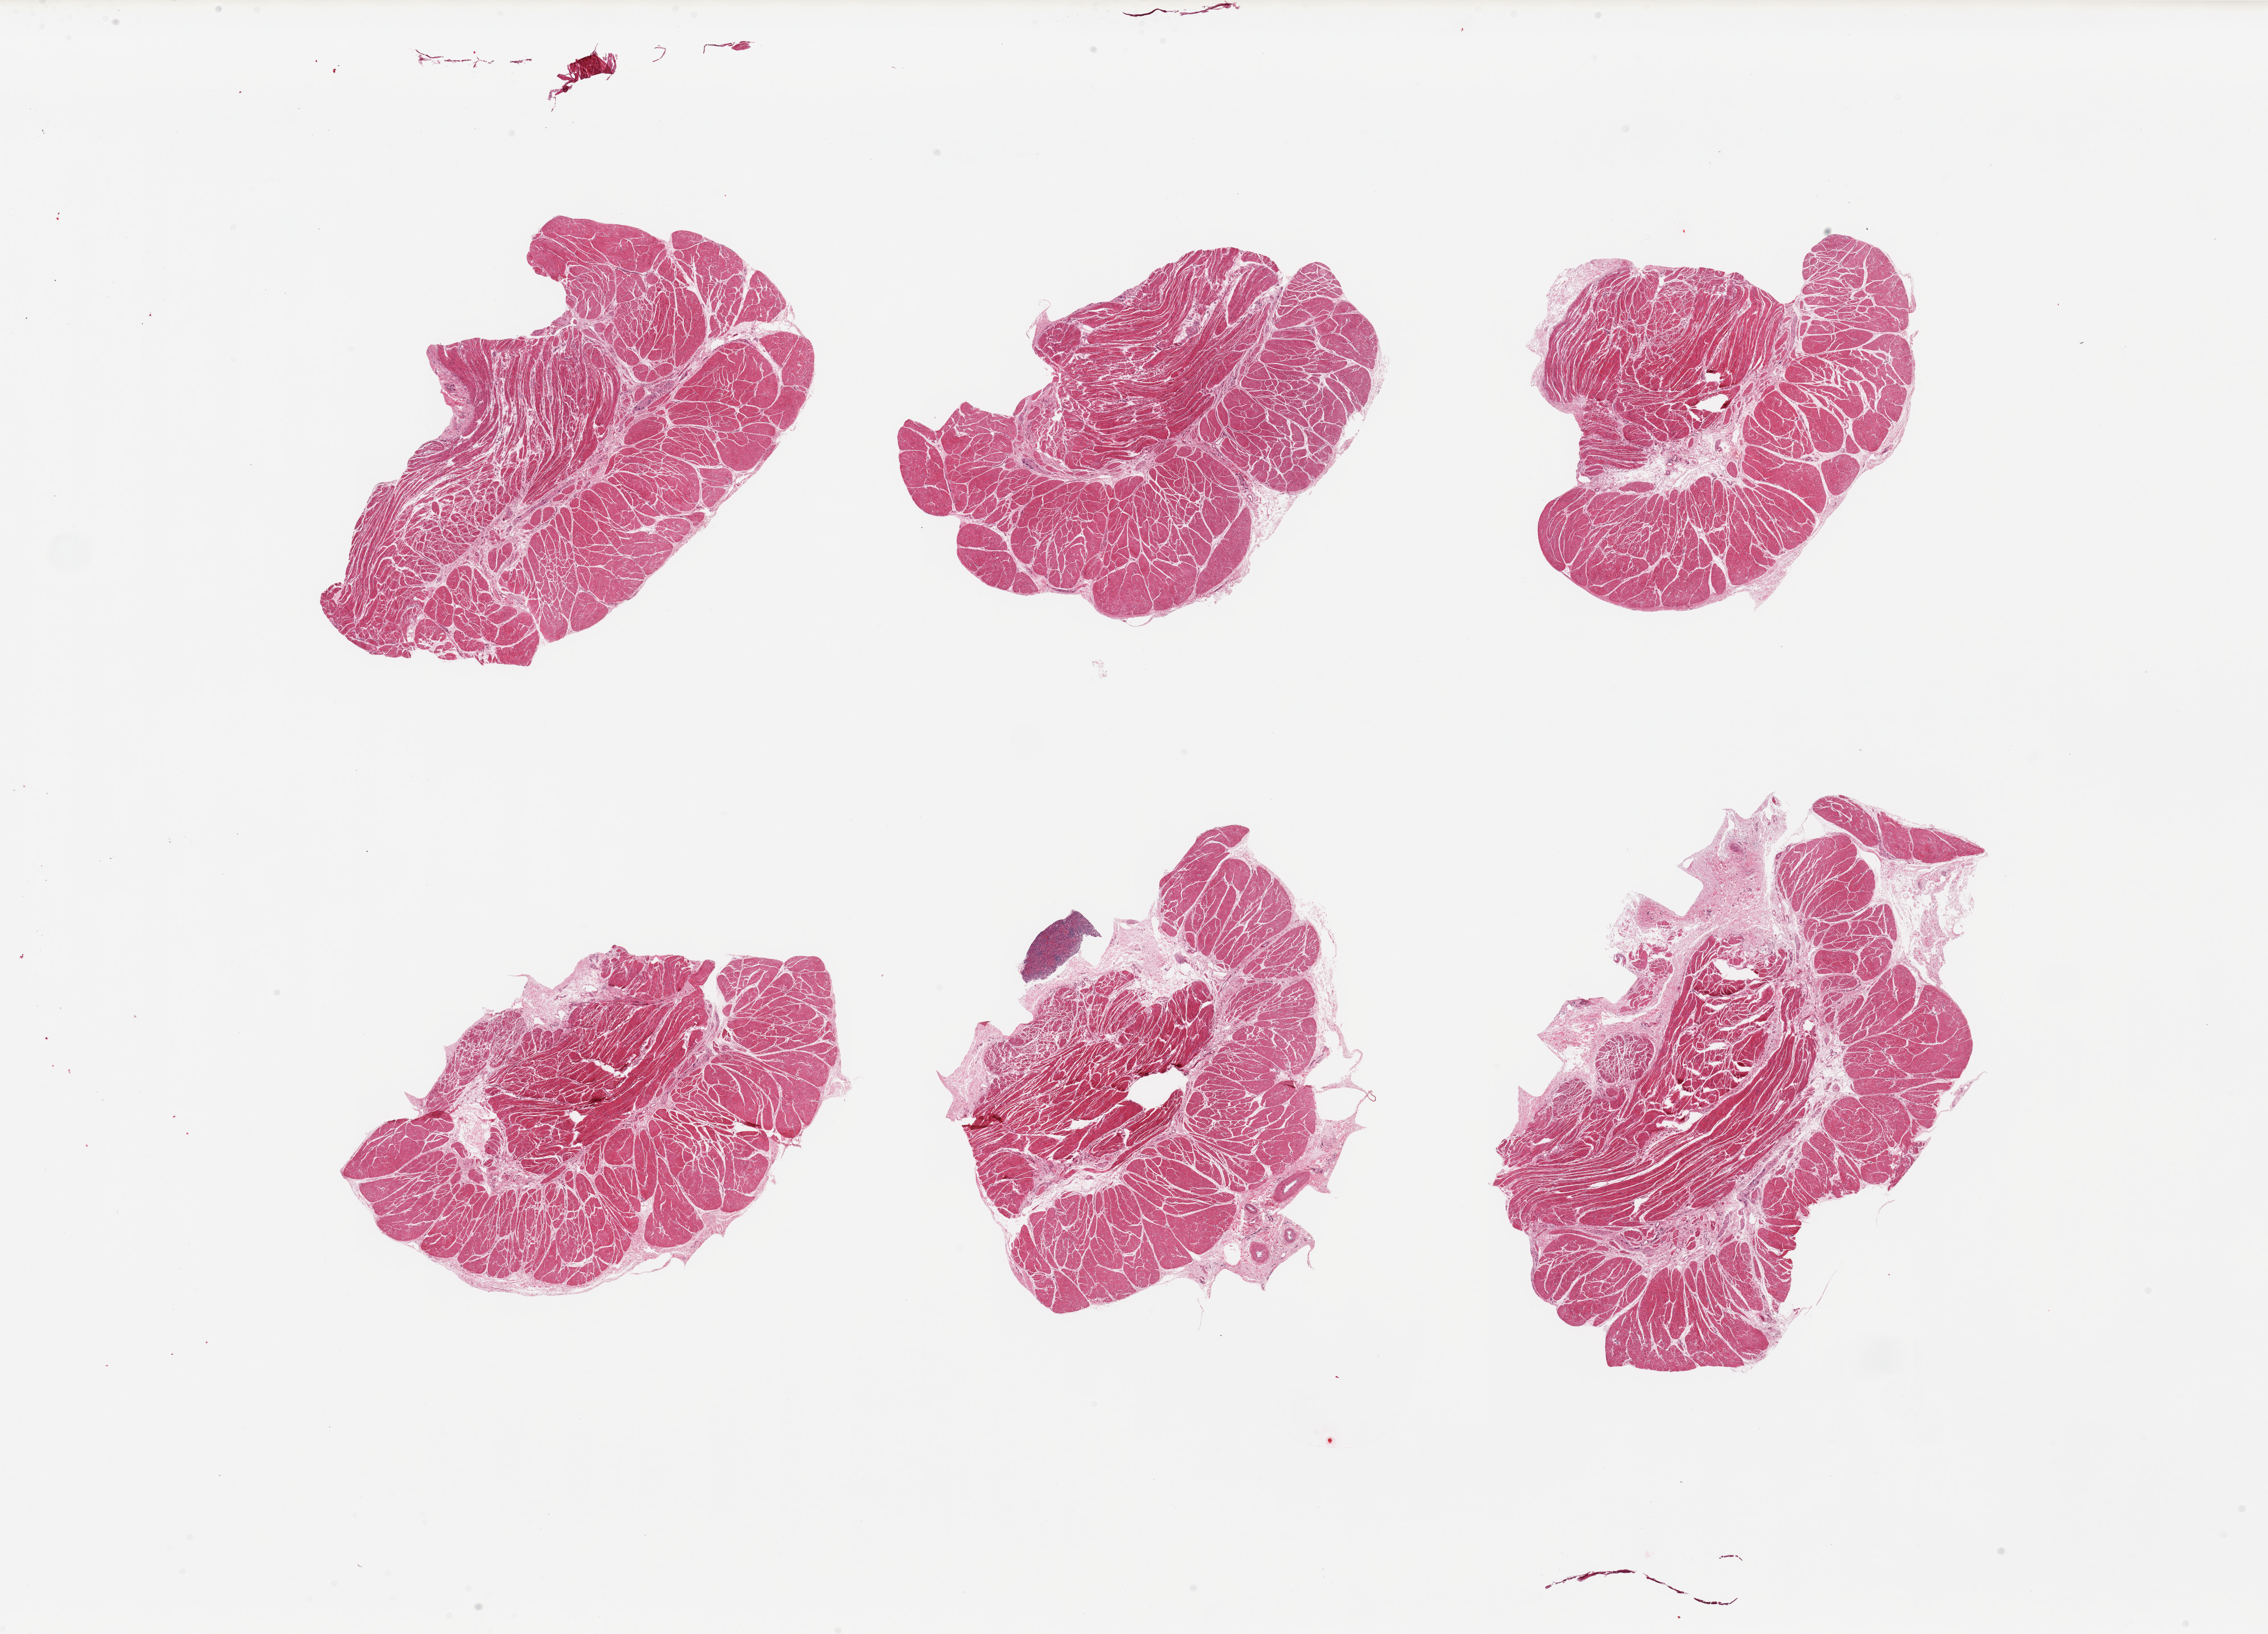
Whole-slide image, haematoxylin and eosin stain, whole scanned area (about 31.5 x 22.7 mm, from a 20x scan) shown as a low-resolution overview; PAXgene-fixed paraffin-embedded (PFPE) section; target tissue: esophageal muscle; tissue donor sample. Female donor.
- reviewer comment on this tissue sample: 6 pieces, target muscularis